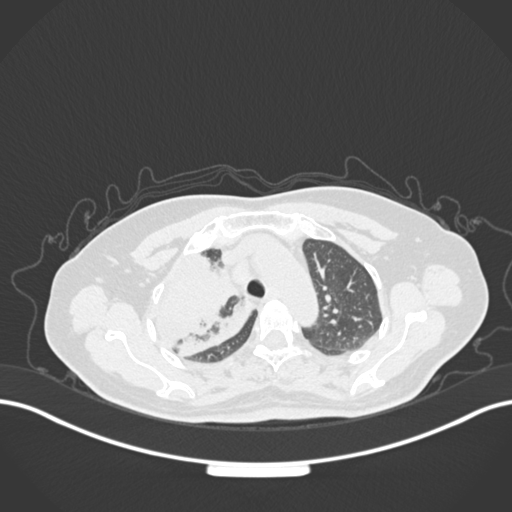
Chest CT, one axial slice. Position 121 of 177 along the scan axis. Reconstruction kernel B30f. 120 kVp. Lung window (W 1500 / L -600 HU). 1 mm slice thickness. 512 × 512 image matrix, field of view 400 × 400 mm. Patient: female, 60 years. From the clinical record (not read from this slice): clinical TNM (as recorded): T3 N1 M1.
Outlined on this slice (rectangle marked by the reading radiologist):
- lung tumour (recorded histology: adenocarcinoma): bounding box (x1, y1, x2, y2) in pixels: (140, 243, 237, 357)